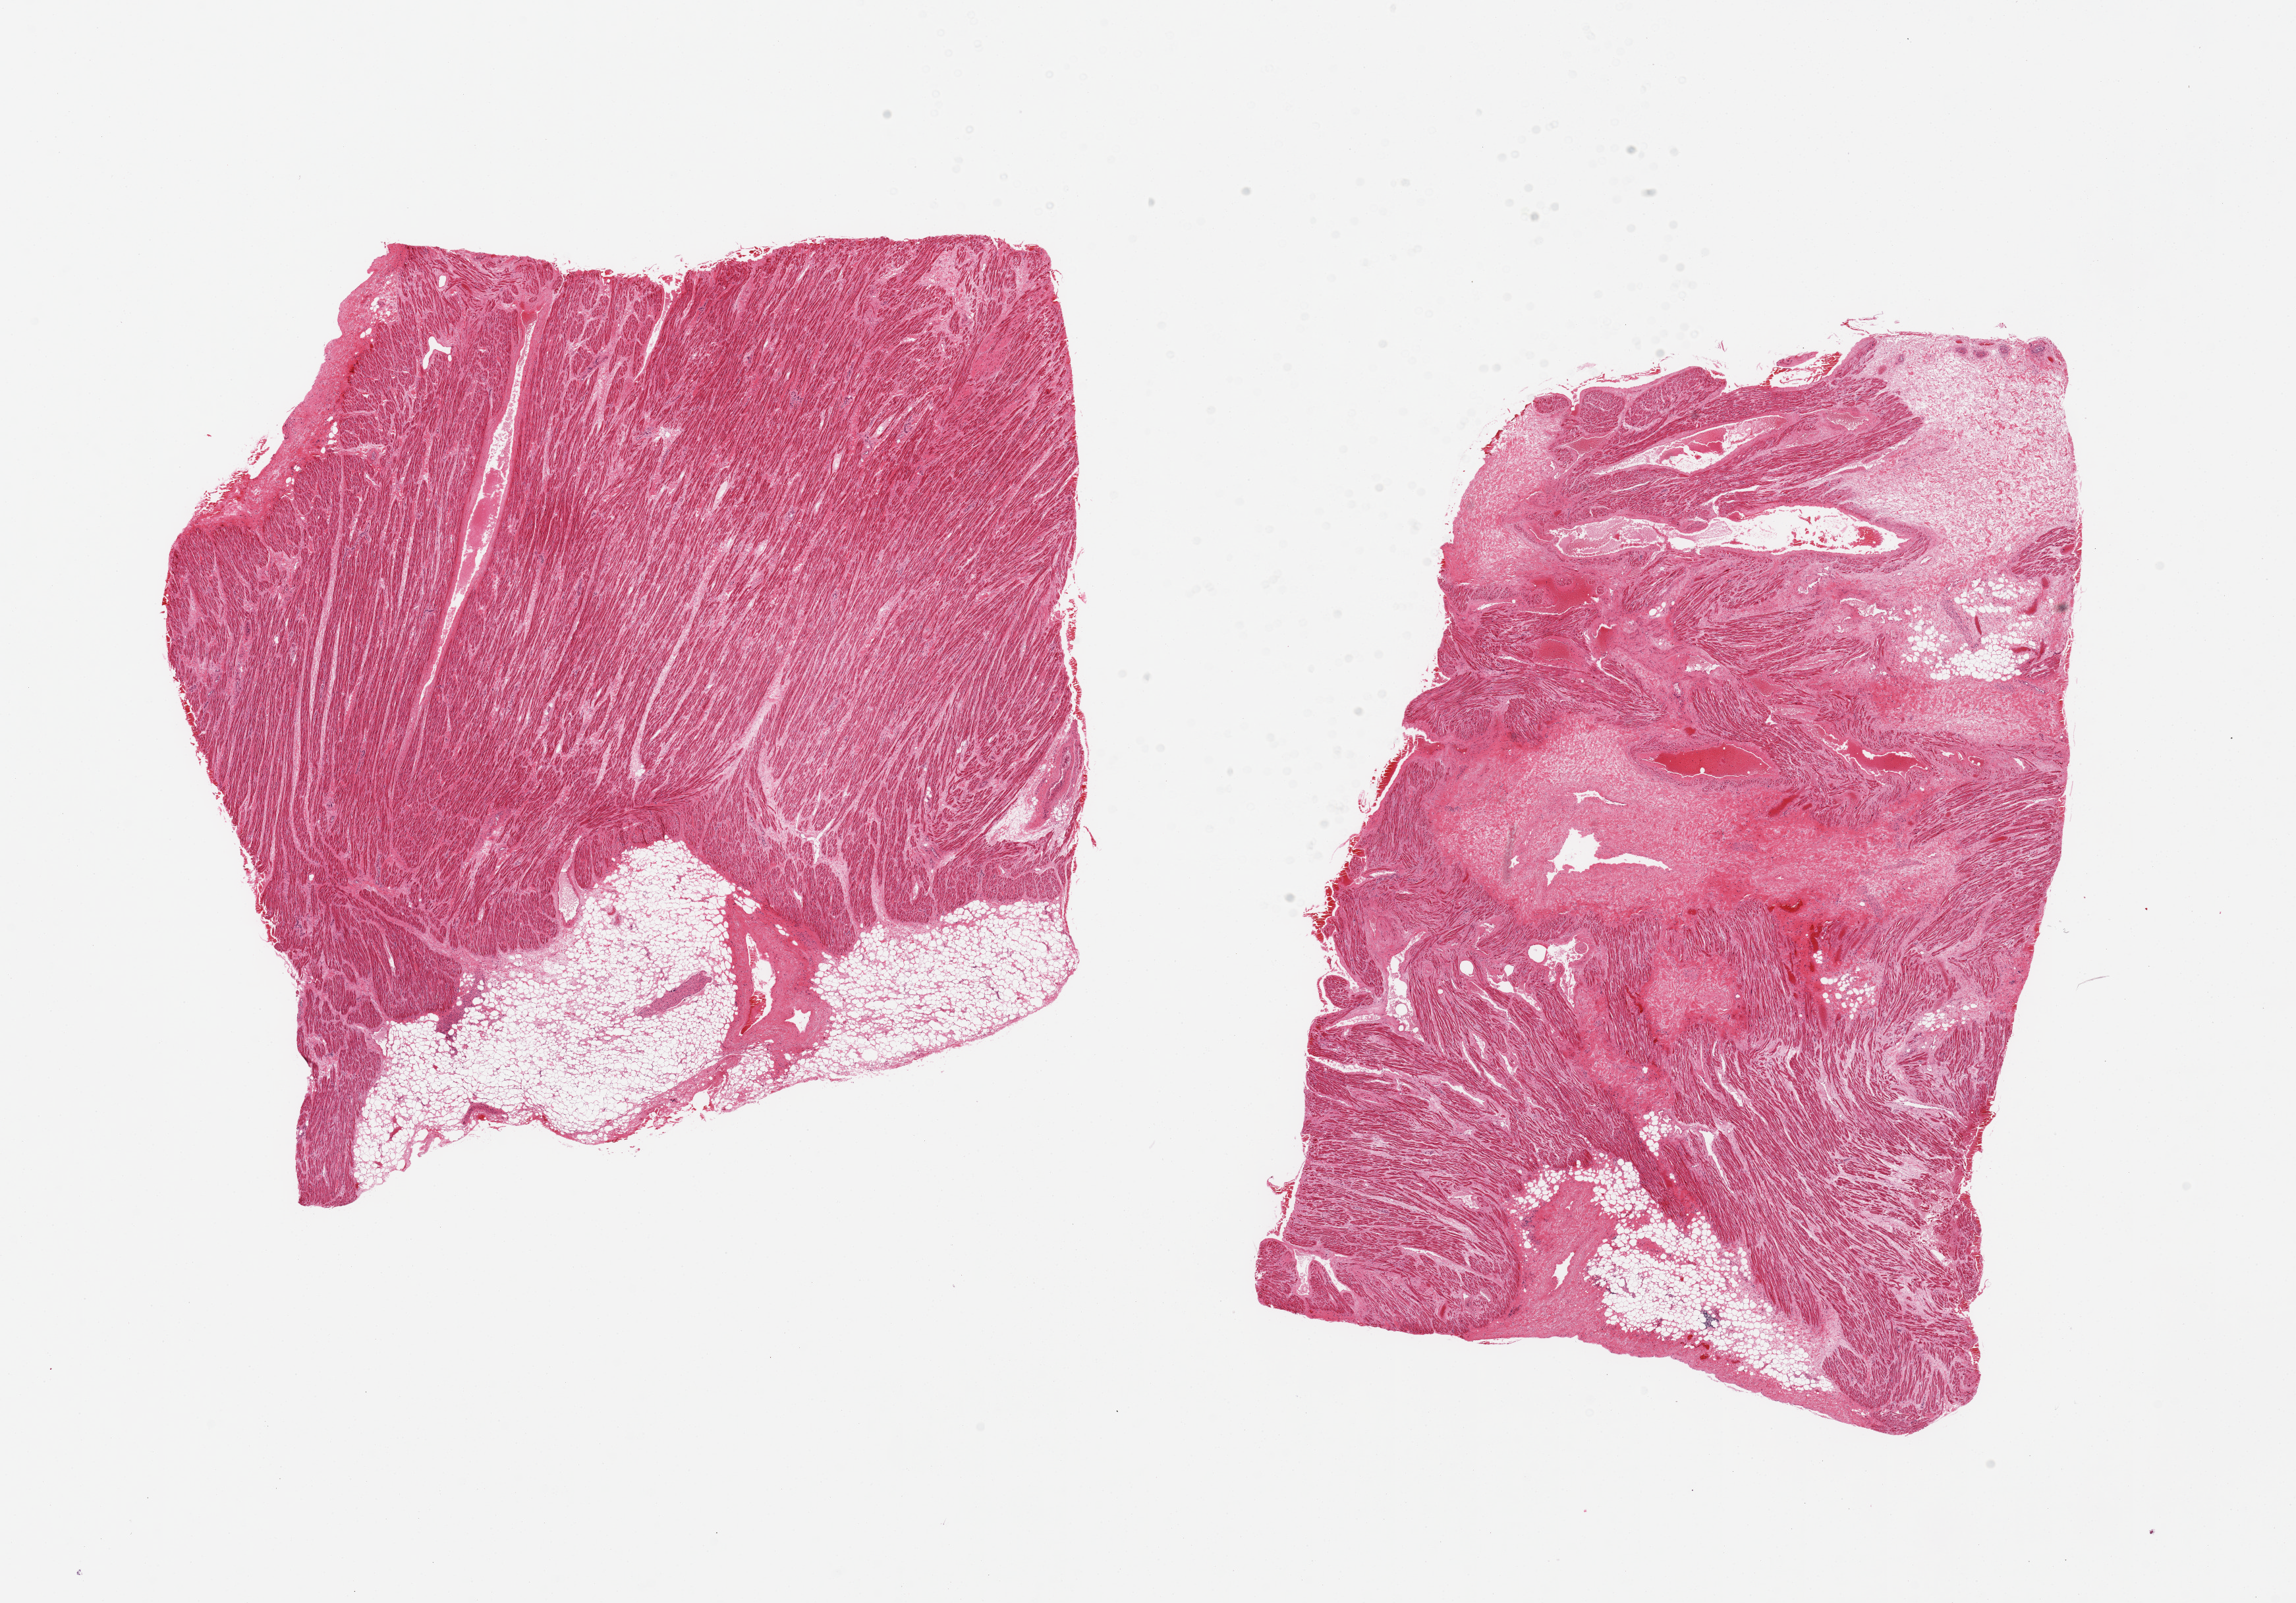
Whole-slide image, hematoxylin and eosin (H&E) stain — a low-resolution overview of the entire scanned area, about 27.6 x 19.2 mm (from a 20x scan). PAXgene-fixed paraffin-embedded (PFPE) section. Section of auricular appendage (target tissue). Donor tissue sample. Donor sex: male.
• reviewer comment on this tissue sample: 2 pieces, some interstitial fibrosis, one piece is 20% fat, second is 40% fat/fibrous